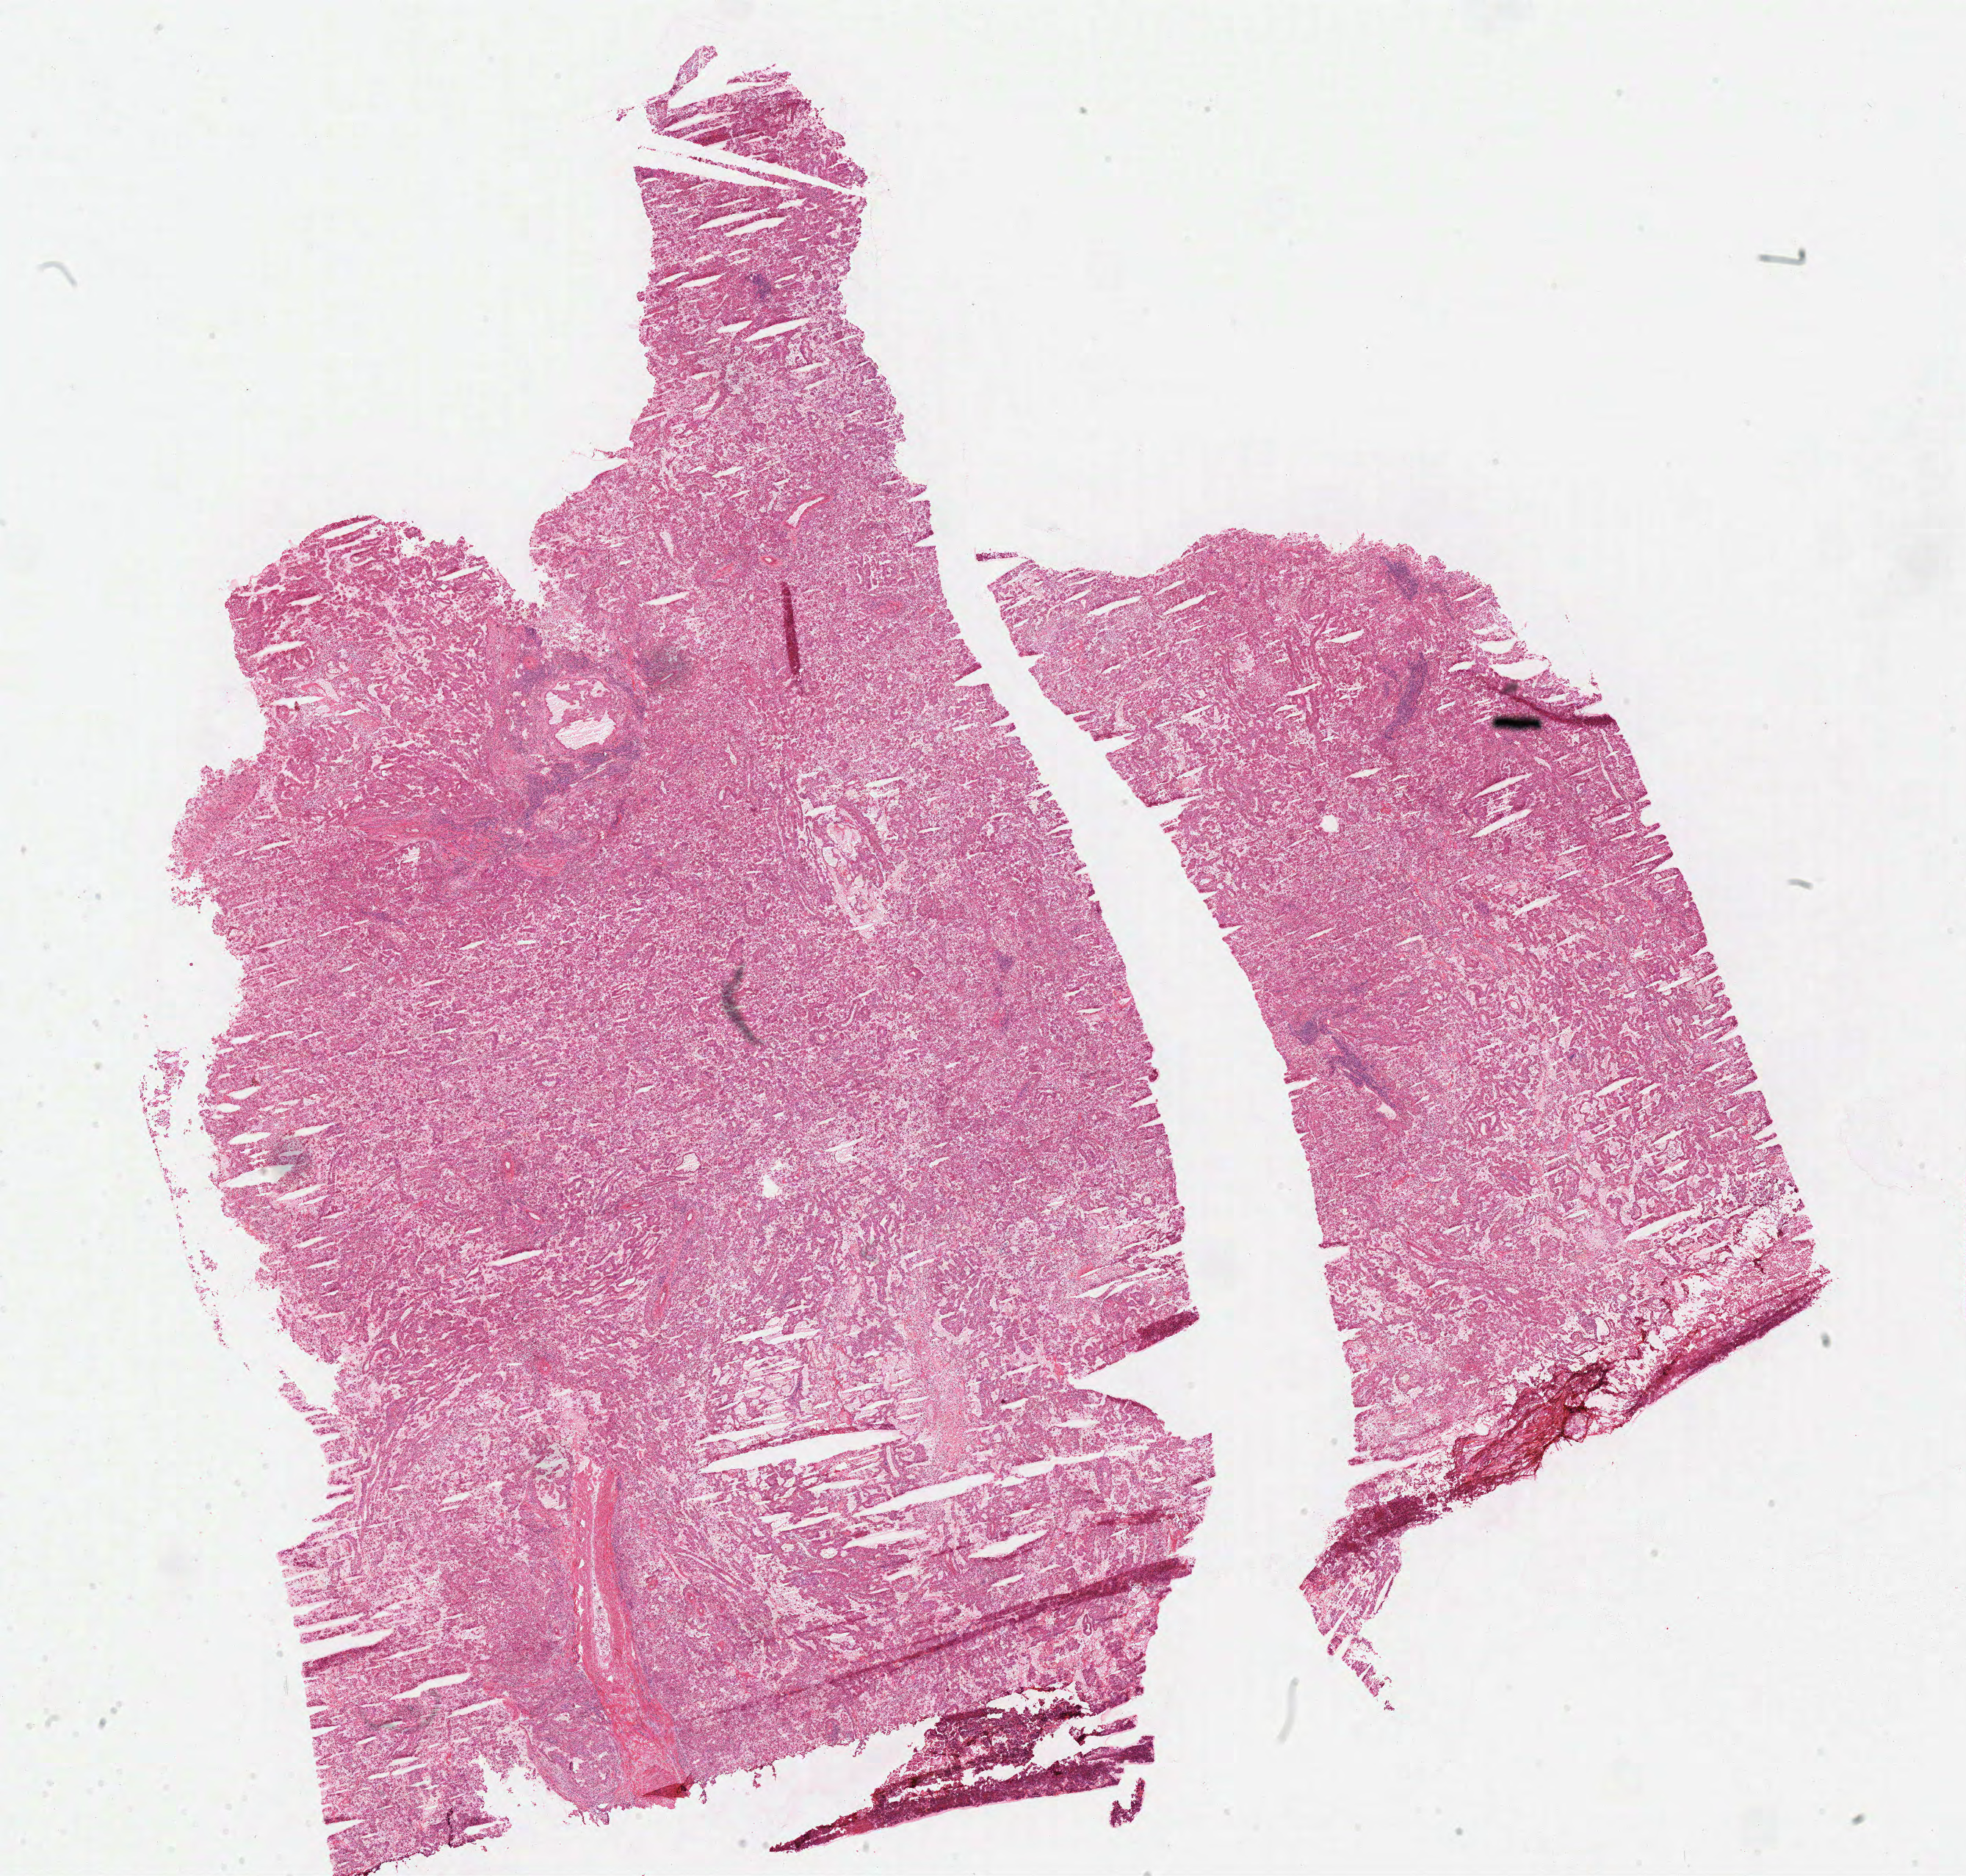
Digitized H&E tissue section (whole slide) — low-resolution overview of the scanned area, about 21.1 x 20.1 mm, frozen section from the top of the tissue portion, kidney, primary tumour sample. Male patient; age at initial diagnosis 54 years. Pathologist review of this section (percent, as recorded): tumour cells 90%, tumour nuclei 80%, normal cells 0%, stromal cells 10%, necrosis 0%.
AJCC pathologic stage: III. Lymph nodes positive (case pathology): 0 of 18 examined. Diagnosis: Papillary adenocarcinoma, NOS.